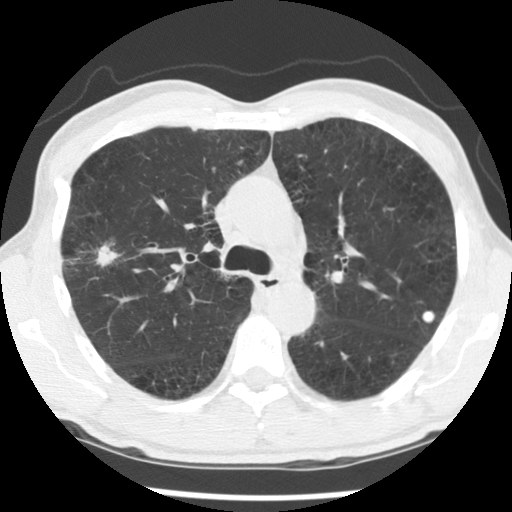
Low-dose screening chest CT, one axial slice; slice 87 of 138 in the series (ordered by position); 140 kVp; lung window (W 1500 / L -600 HU); 512 × 512 image matrix.
Outlined on this slice (expert manual segmentation):
- lesion 1 (tumor, upper lobe of right lung): bounding box (x1, y1, x2, y2) in pixels: (96, 243, 121, 267)